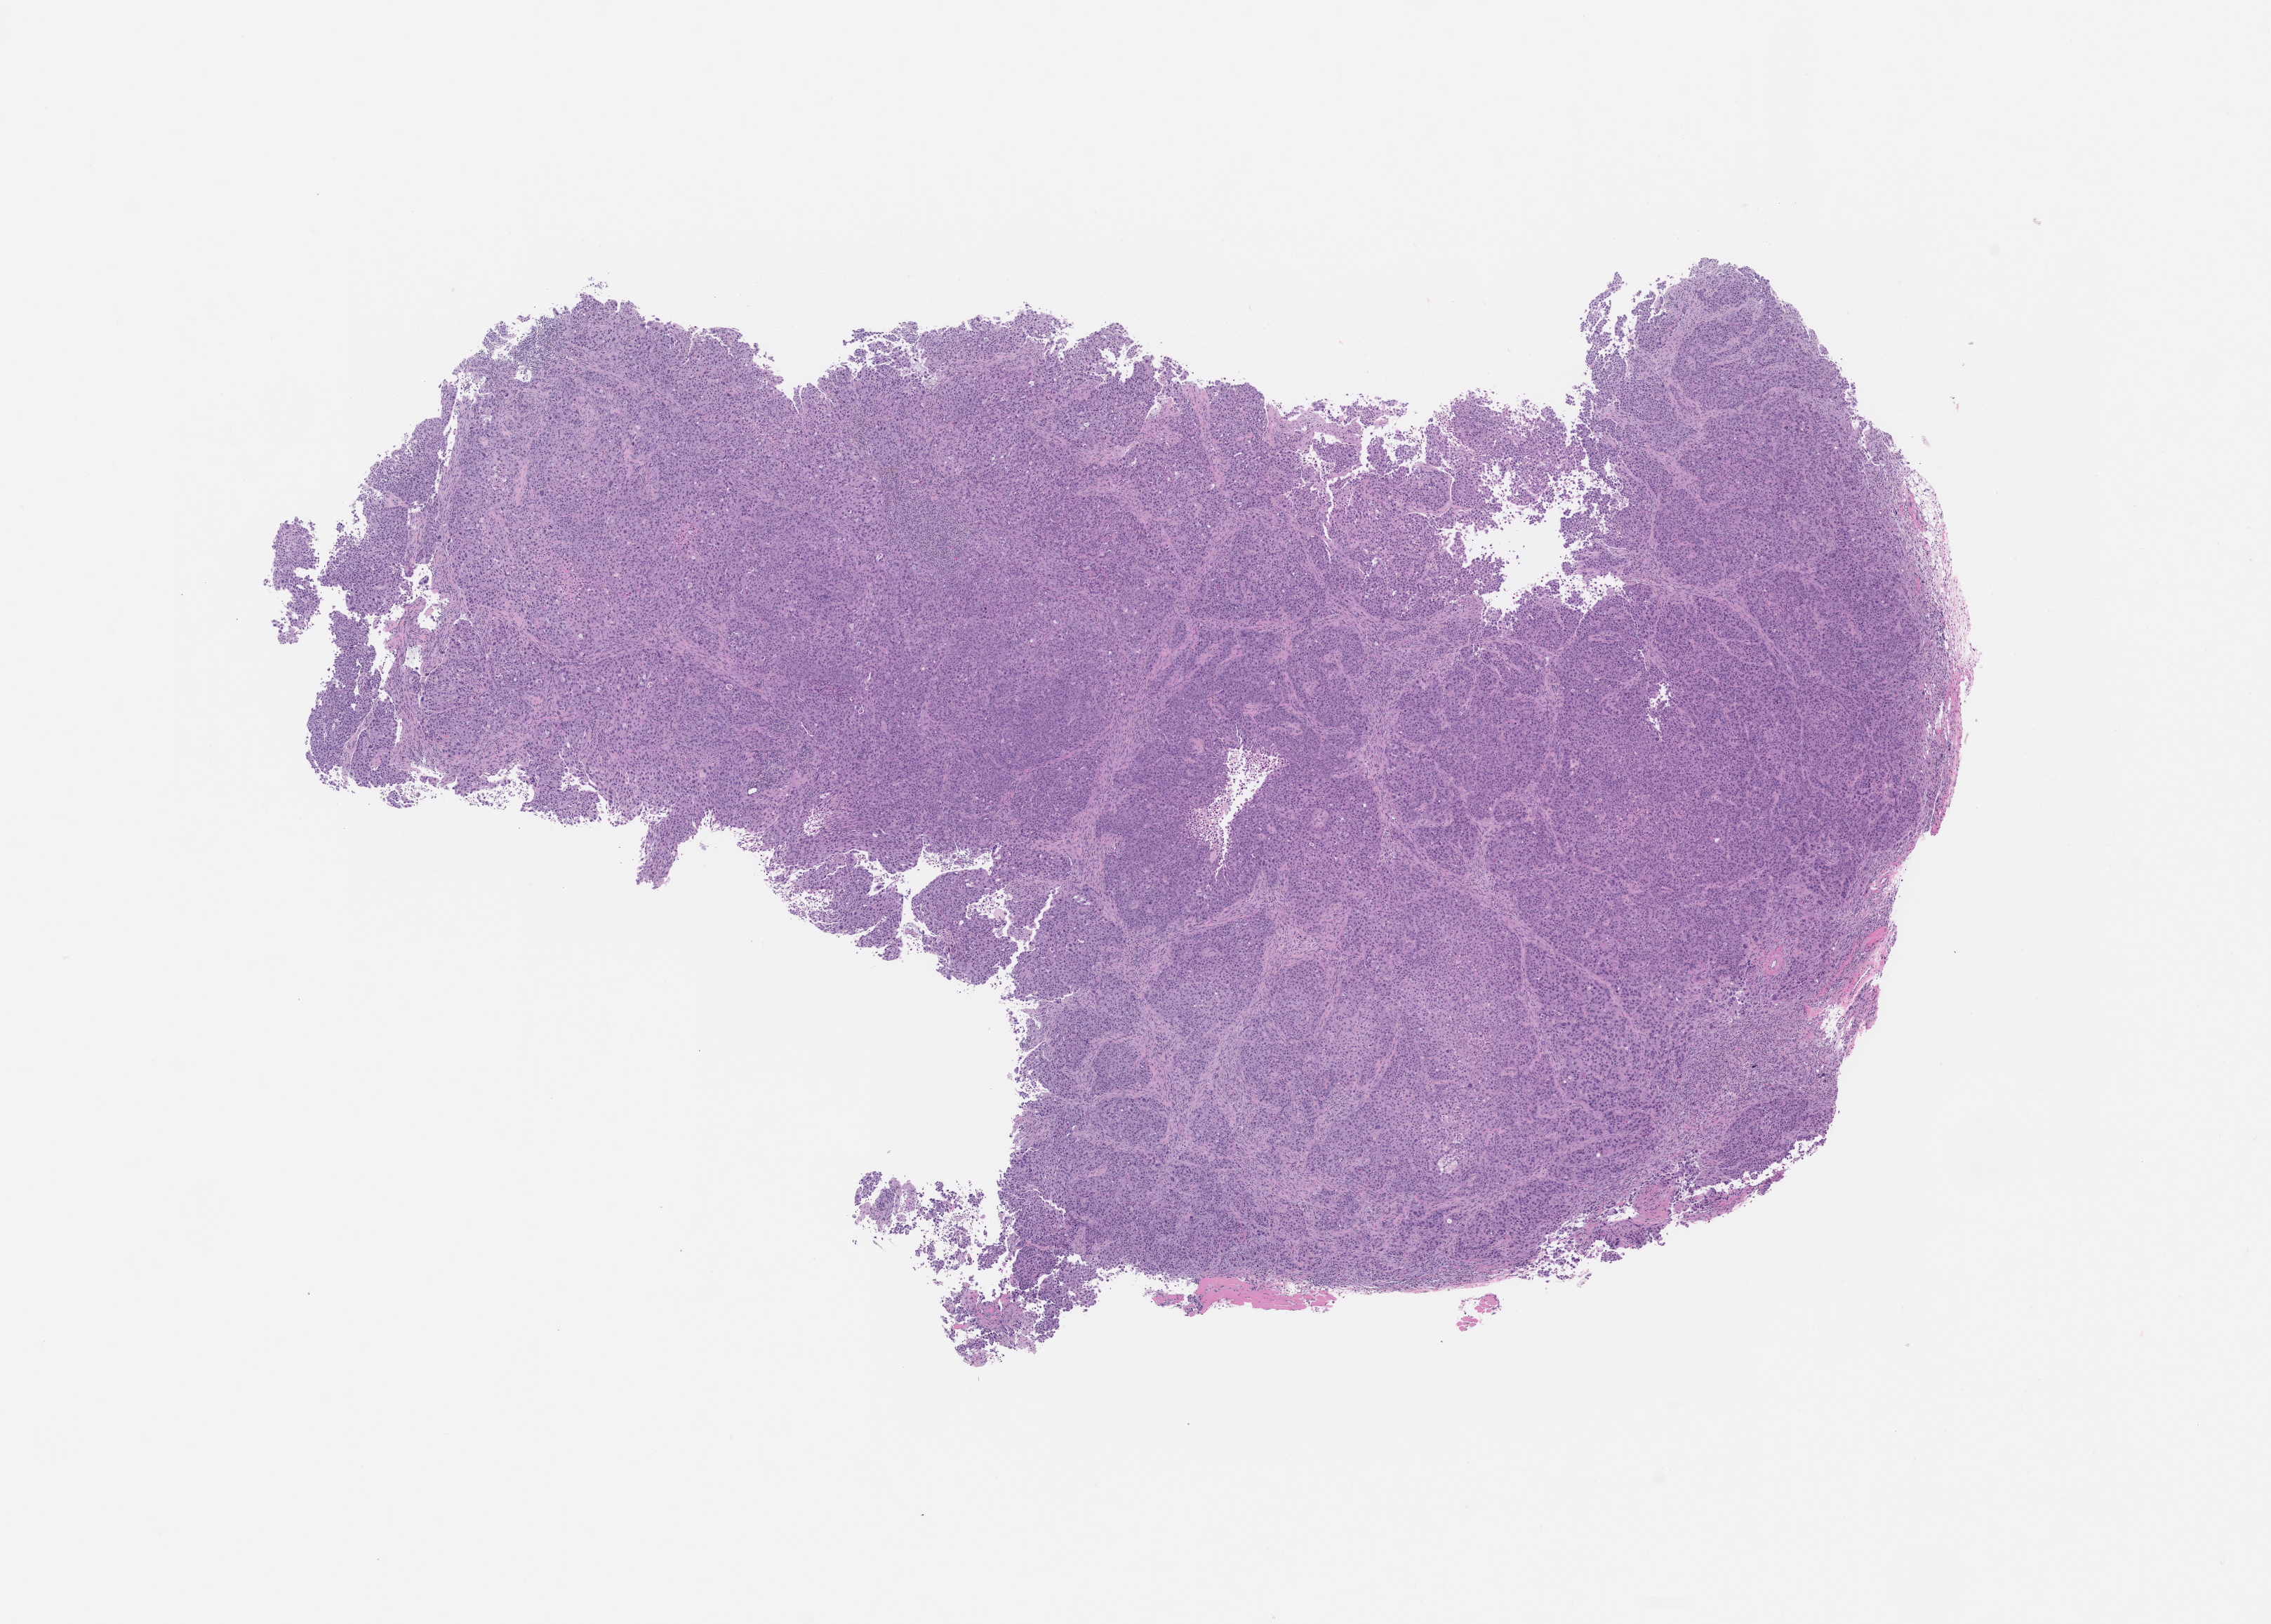
Haematoxylin and eosin whole-slide image of a patient-derived xenograft (PDX) tumor grown in a mouse, passage 1, whole scanned area (about 13.0 x 9.3 mm) shown as a low-resolution overview, FFPE section, tumor site category: lung.
Originating patient diagnosis: Lung Adenocarcinoma.